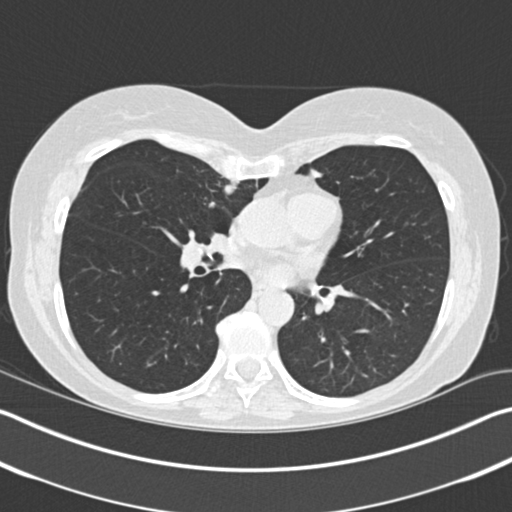
Low-dose screening chest CT, one axial slice; position 94 of 183 along the scan axis; reconstruction kernel B30f; 120 kVp; lung window (W 1500 / L -600 HU); 2 mm slice thickness; 512 × 512 image matrix, field of view 340 × 340 mm.
Structures marked on this image (manually delineated by an expert):
- lesion 1 (tumor, upper lobe of right lung): bounding box <224,179,240,194> (left, top, right, bottom; pixels)